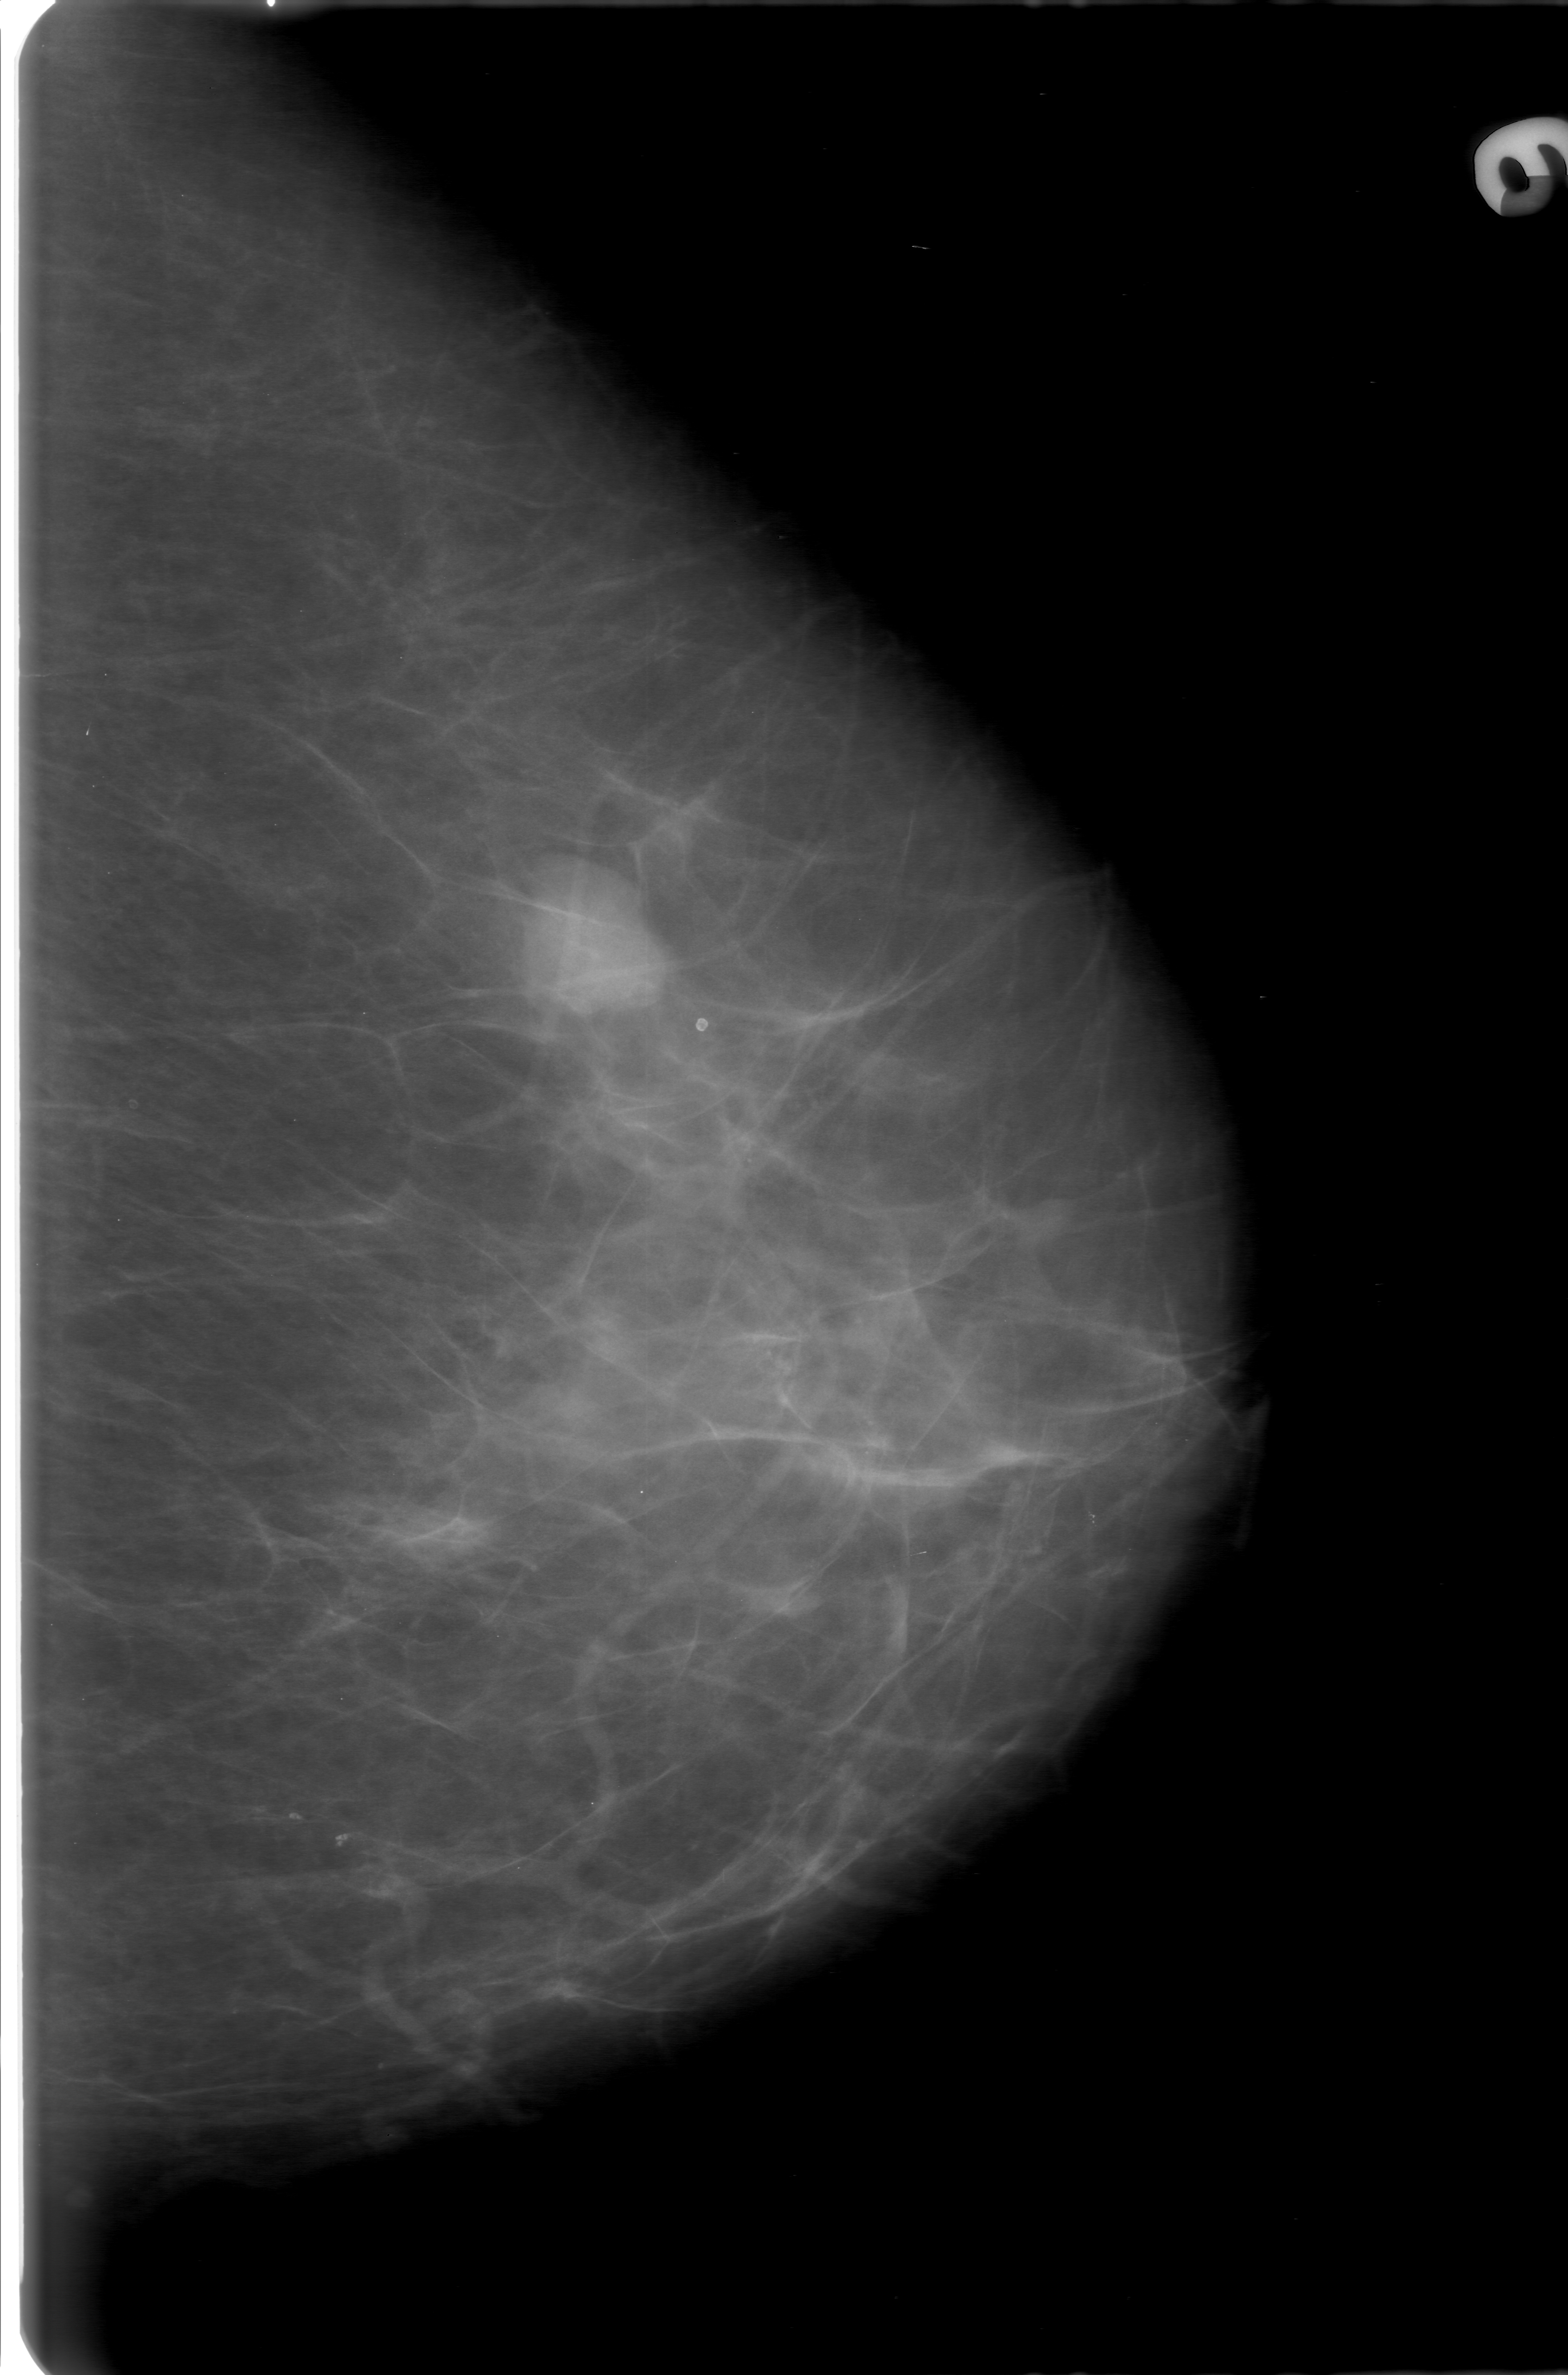
Digitized screen-film mammogram; left breast; CC view; breast composition: almost entirely fatty (BI-RADS density category 1 of 4).
- Finding: mass, shape lobulated, margins circumscribed; BI-RADS assessment category 0 (incomplete: needs additional imaging); subtlety rating 5 on a 1 (subtle) to 5 (obvious) scale; pathology (as recorded): benign.